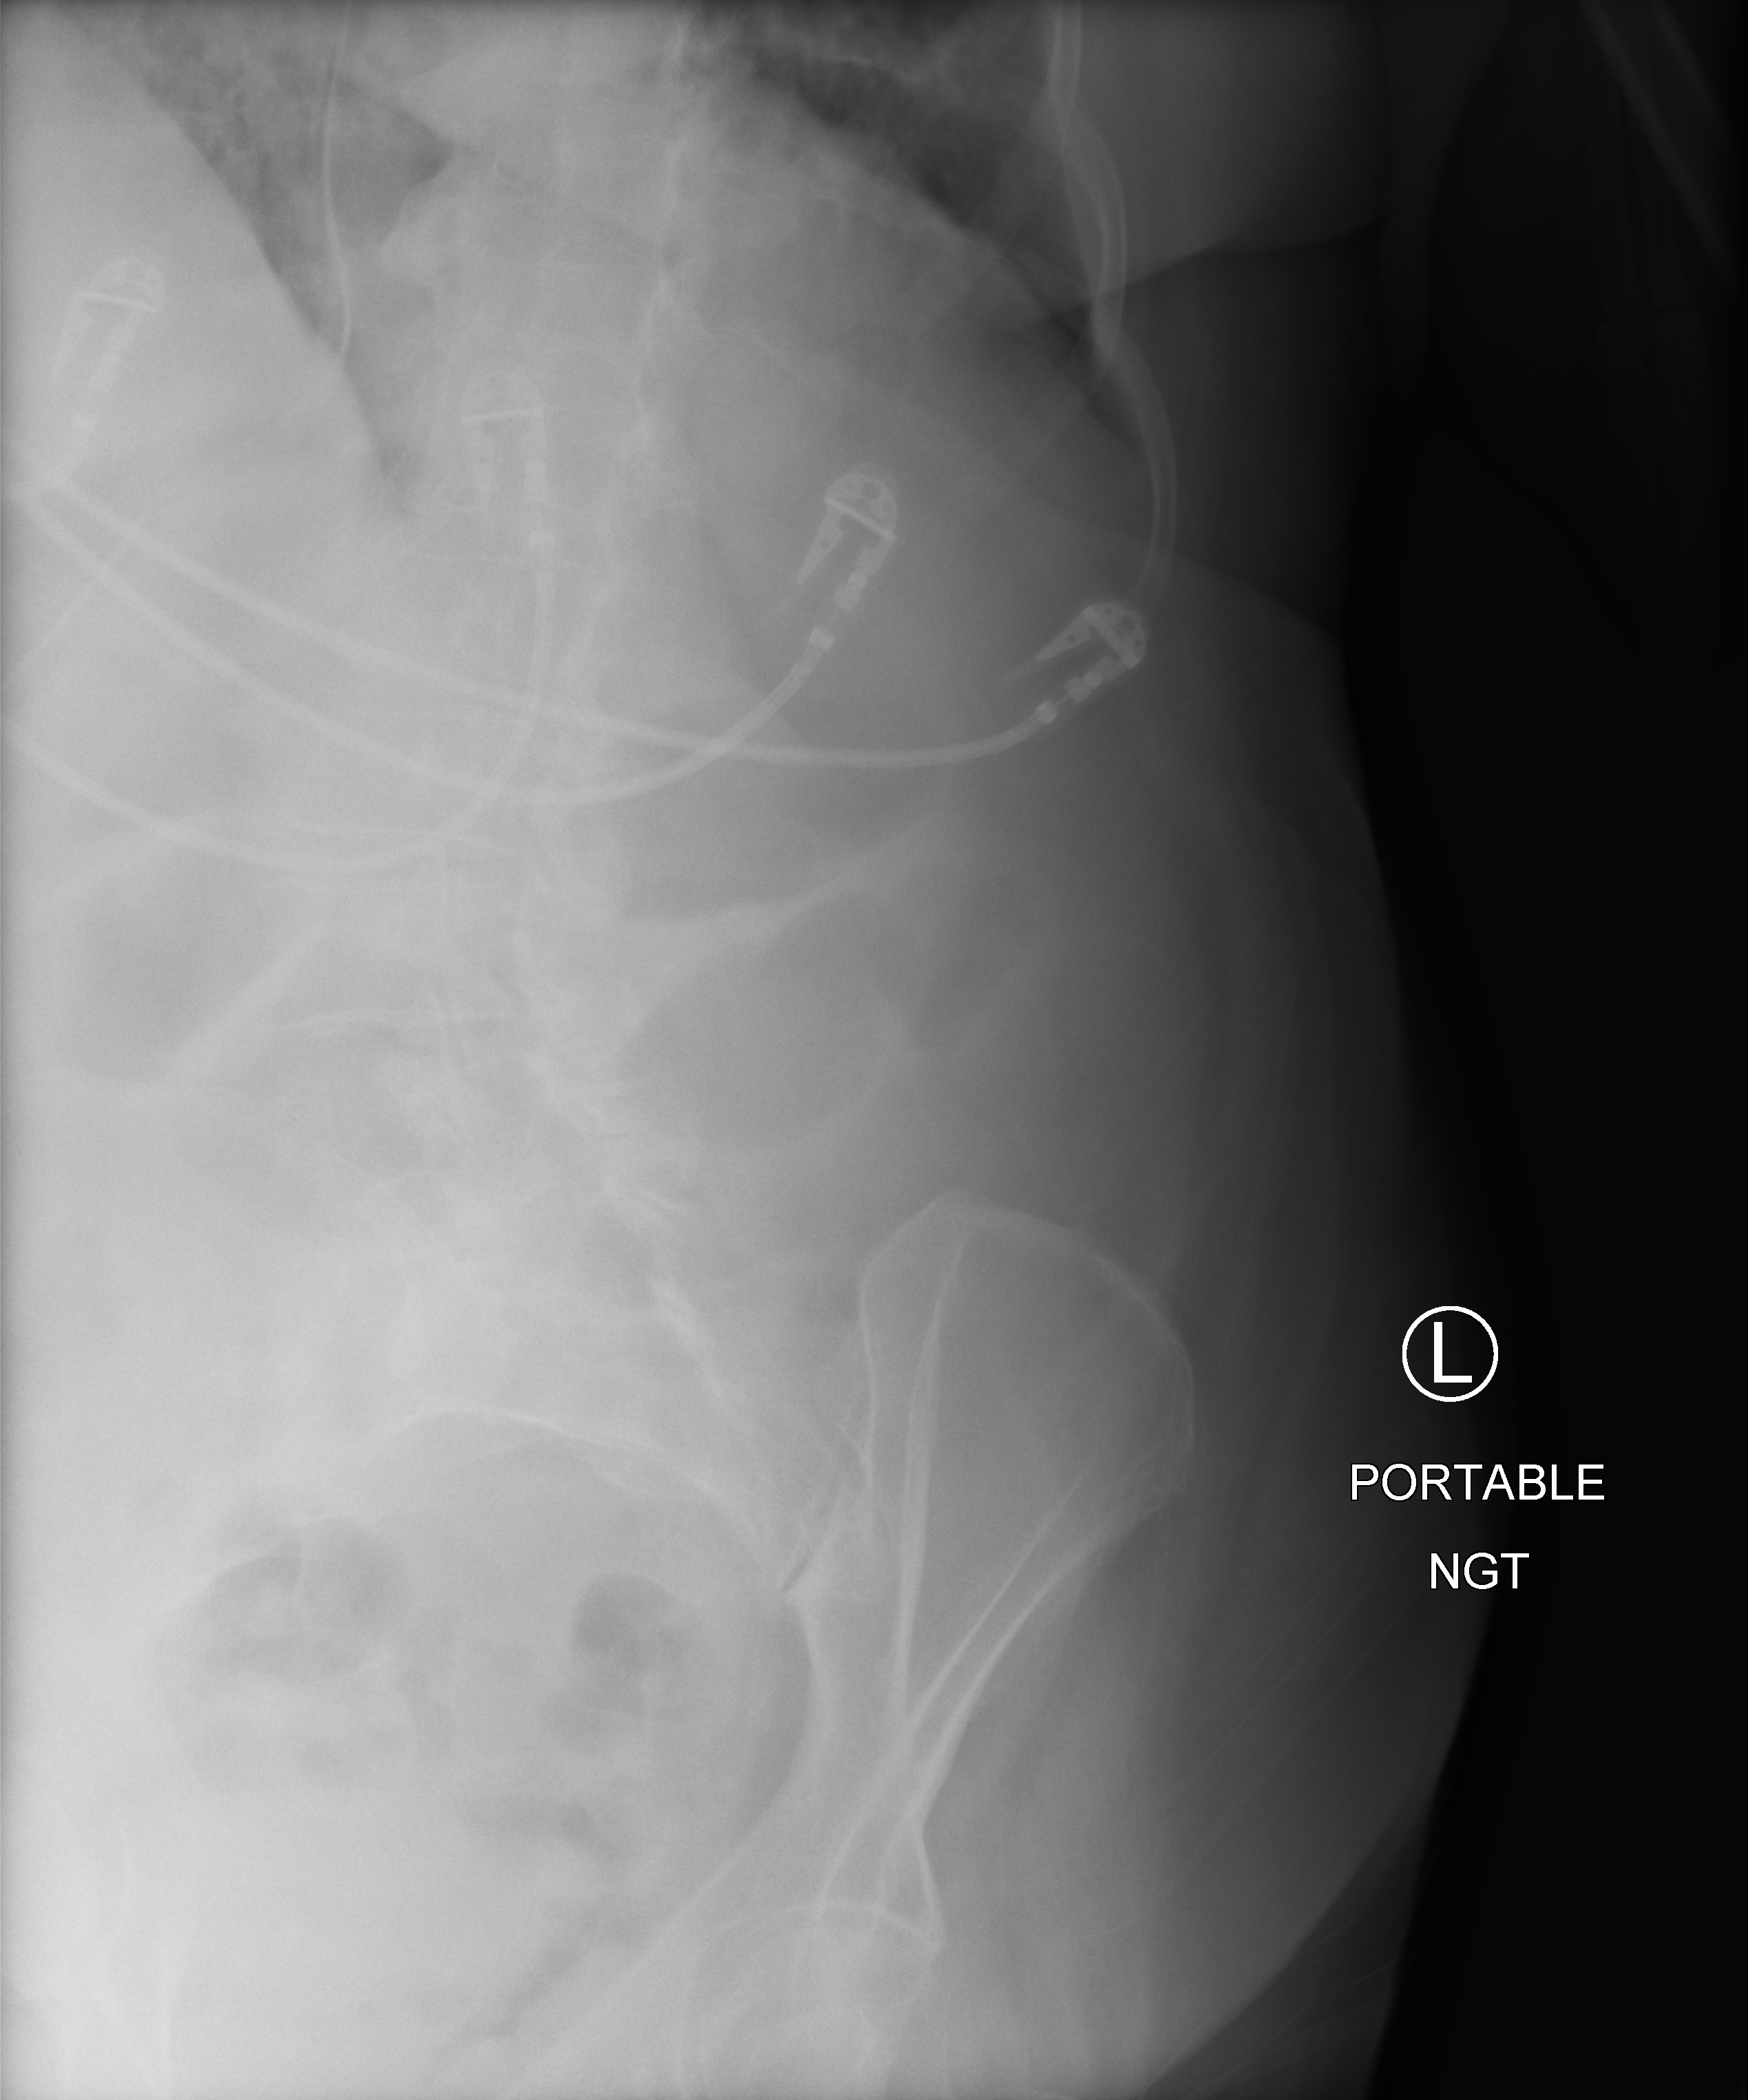
Bedside abdomen radiograph (computed radiography); anteroposterior (AP) projection. Patient hospitalised with COVID-19; female, aged 75–90 years.
Hospital-stay facts (about this admission, not read from this image; timing relative to this image not recorded): COPD (admission record): yes.